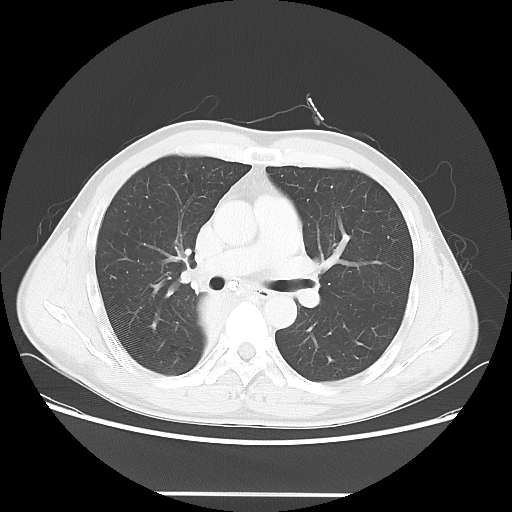
Chest CT, one axial slice. Position 37 of 62 along the scan axis. 120 kVp. Lung window (W 1500 / L -600 HU). 512 × 512 image matrix, field of view 393 × 393 mm. Patient: male, 47 years. From the clinical record (not read from this slice): clinical TNM (as recorded): T2 N0 M0.
Outlined on this slice (bounding box drawn by a radiologist):
- lung tumour (recorded histology: squamous cell carcinoma): bounding box [x1, y1, x2, y2] px = [194, 287, 234, 341]